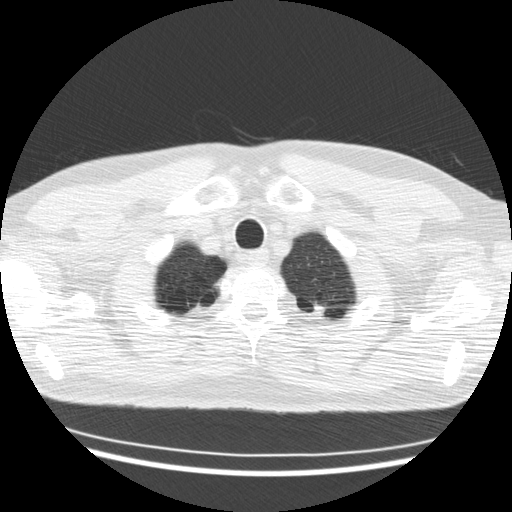
Low-dose screening chest CT, one axial slice; slice 159 of 176 in the series (ordered by position); lung window (W 1500 / L -600 HU); 512 × 512 image matrix.
Annotated regions visible in this slice (expert manual segmentation):
- lesion 1 (tumor, upper lobe of left lung): bounding box [x1, y1, x2, y2] px = [312, 305, 326, 316]